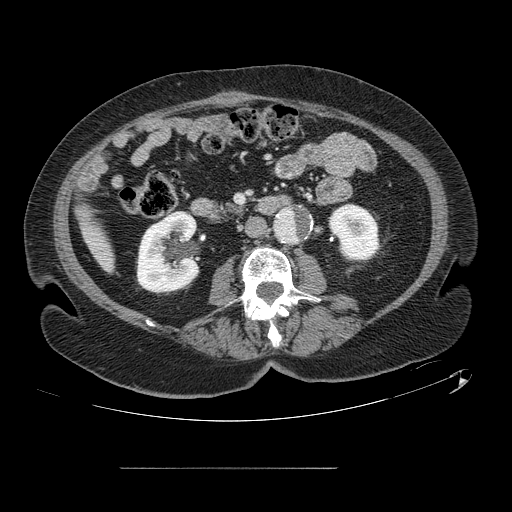
Contrast-enhanced abdominal CT, one axial slice. Position 26 of 148 along the scan axis. Intravenous contrast given. Soft-tissue window (W 400 / L 40 HU). 2.5 mm slice thickness. 512 × 512 image matrix, field of view 439 × 439 mm. Female patient, age 75 years. From the clinical record (not read from this slice): diagnosis: colorectal cancer liver metastases, imaged before liver resection; multiple liver metastases: no.
Annotated regions visible in this slice (expert manual segmentation):
- liver: box from (x=83, y=219) to (x=114, y=270) px
- planned liver remnant (the part of the liver to remain after resection): (x=84, y=220)–(x=114, y=269)